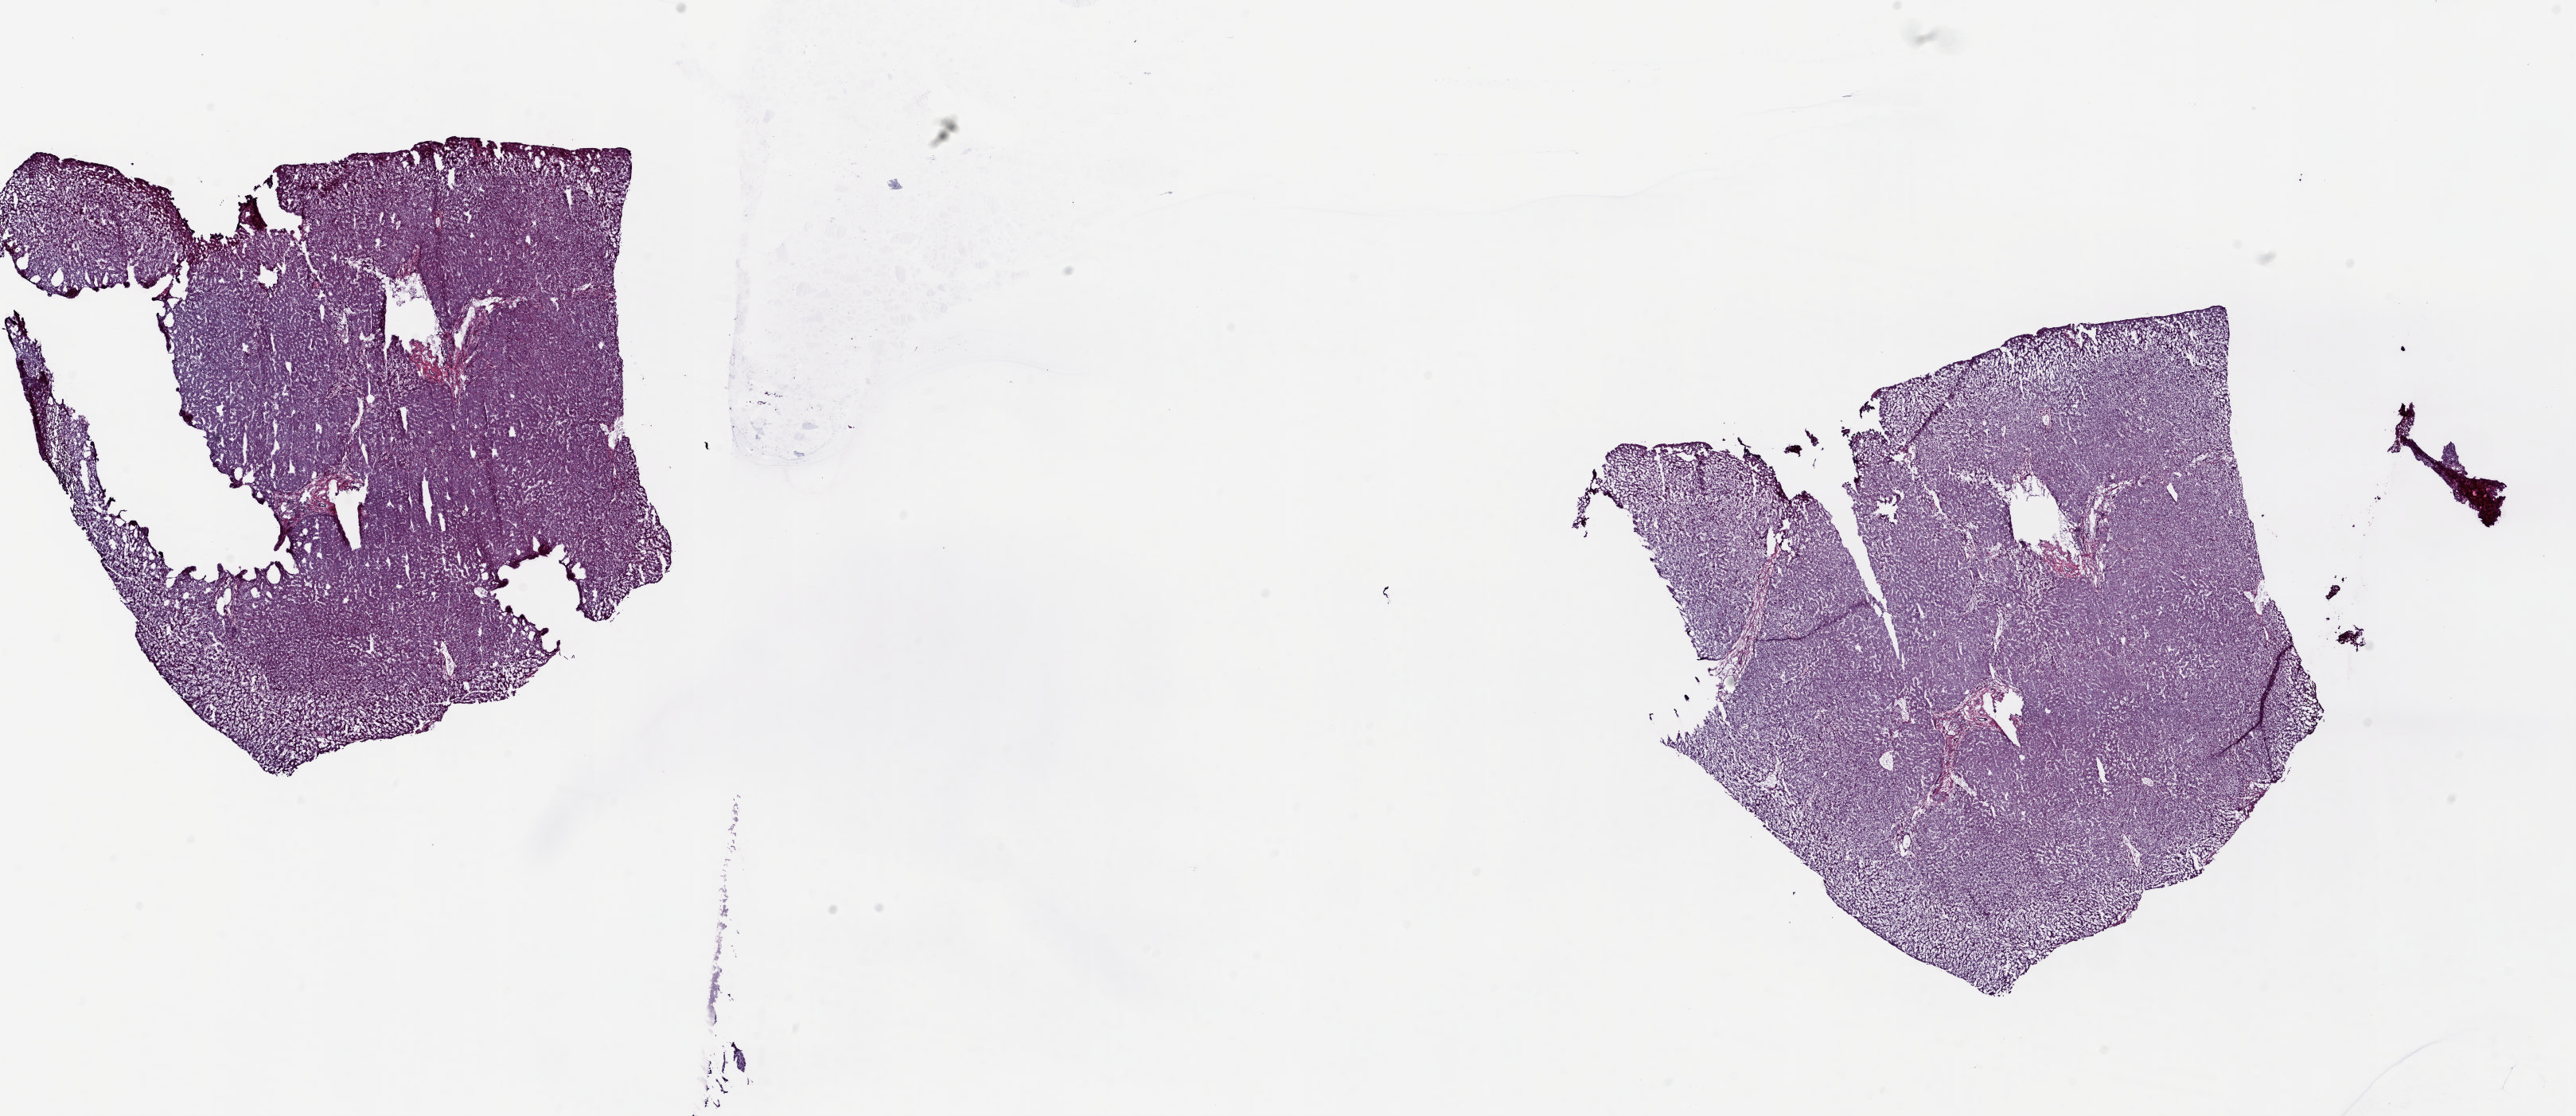
H&E-stained whole-slide image — whole scanned area (about 25.7 x 11.1 mm, from a 20x scan) shown as a low-resolution overview; frozen section; solid tissue normal (non-tumour tissue) sample from the liver. Male patient; age at initial diagnosis 40 years. Pathologist review of this section (percent, as recorded): tumour cells 0%, tumour nuclei 0%, normal cells 95%, stromal cells 5%, necrosis 0%. Infiltration values recorded for this section: lymphocyte infiltration 1%, monocyte infiltration 0%, neutrophil infiltration 0%.
This section: solid tissue normal (non-tumour) sample from the same patient. Patient diagnosis: Hepatocellular carcinoma, NOS.